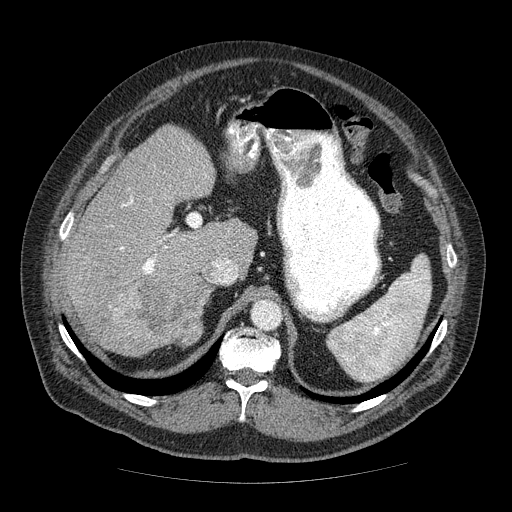
Contrast-enhanced abdominal CT (liver protocol), one axial slice. Reconstruction kernel STANDARD. Soft-tissue window (W 400 / L 40 HU). 512 × 512 image matrix, field of view 420 × 420 mm. Case-level facts recorded for this patient, not image findings: diagnosis: hepatocellular carcinoma (patient treated with transarterial chemoembolisation; whether this scan precedes or follows treatment is not stated here); TNM stage (as recorded): Stage-IIIA; Child-Pugh class: A; tumour nodularity: multinodular; tumour size: 7 cm.
Structures marked on this image (semi-automatically segmented with operator editing):
- liver parenchyma outside the tumour (the mass and vessels are separate outlines, so this box may not span the whole liver): bounding box (x1, y1, x2, y2) in pixels: (64, 126, 256, 352)
- mass: (85, 273, 203, 357)
- liver vessels: (120, 198, 238, 274)